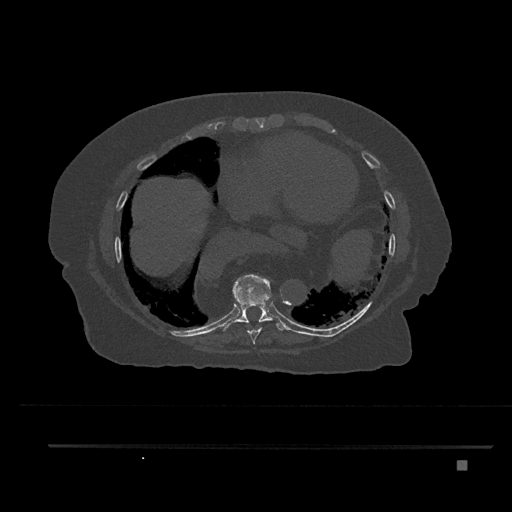
CT including the spine, one axial slice; slice 418 of 797 in the series (ordered by position); 120 kVp; bone window (W 1800 / L 400 HU); 0.5 mm slice thickness; 512 × 512 image matrix. Patient: female, 76 years. From the clinical record (not read from this slice): primary cancer: lung.
Annotated regions visible in this slice (semi-automatically segmented with operator editing):
- T8 vertebra: bounding box (x1, y1, x2, y2) in pixels: (246, 326, 263, 346)
- T9 vertebra: (222, 274, 287, 331)